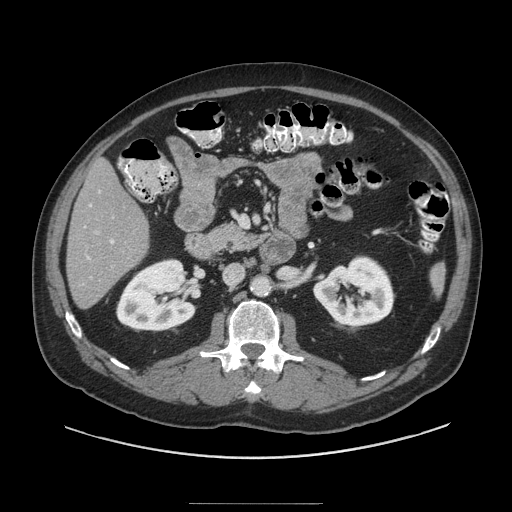
Contrast-enhanced abdominal CT (liver protocol), one axial slice. Position 37 of 91 along the scan axis. Reconstruction kernel STANDARD. Soft-tissue window (W 400 / L 40 HU). 2.5 mm slice thickness. 512 × 512 image matrix, field of view 440 × 440 mm. From the clinical record (not read from this slice): diagnosis: hepatocellular carcinoma (patient treated with transarterial chemoembolisation; whether this scan precedes or follows treatment is not stated here); TNM stage (as recorded): Stage-I; Child-Pugh class: A; tumour nodularity: uninodular; tumour size: 4 cm.
Structures marked on this image (semi-automatic segmentation, software-assisted and operator-edited):
- liver parenchyma outside the tumour (the mass and vessels are separate outlines, so this box may not span the whole liver): box from (x=66, y=160) to (x=148, y=308) px
- liver vessels: (x=87, y=190)–(x=115, y=260)